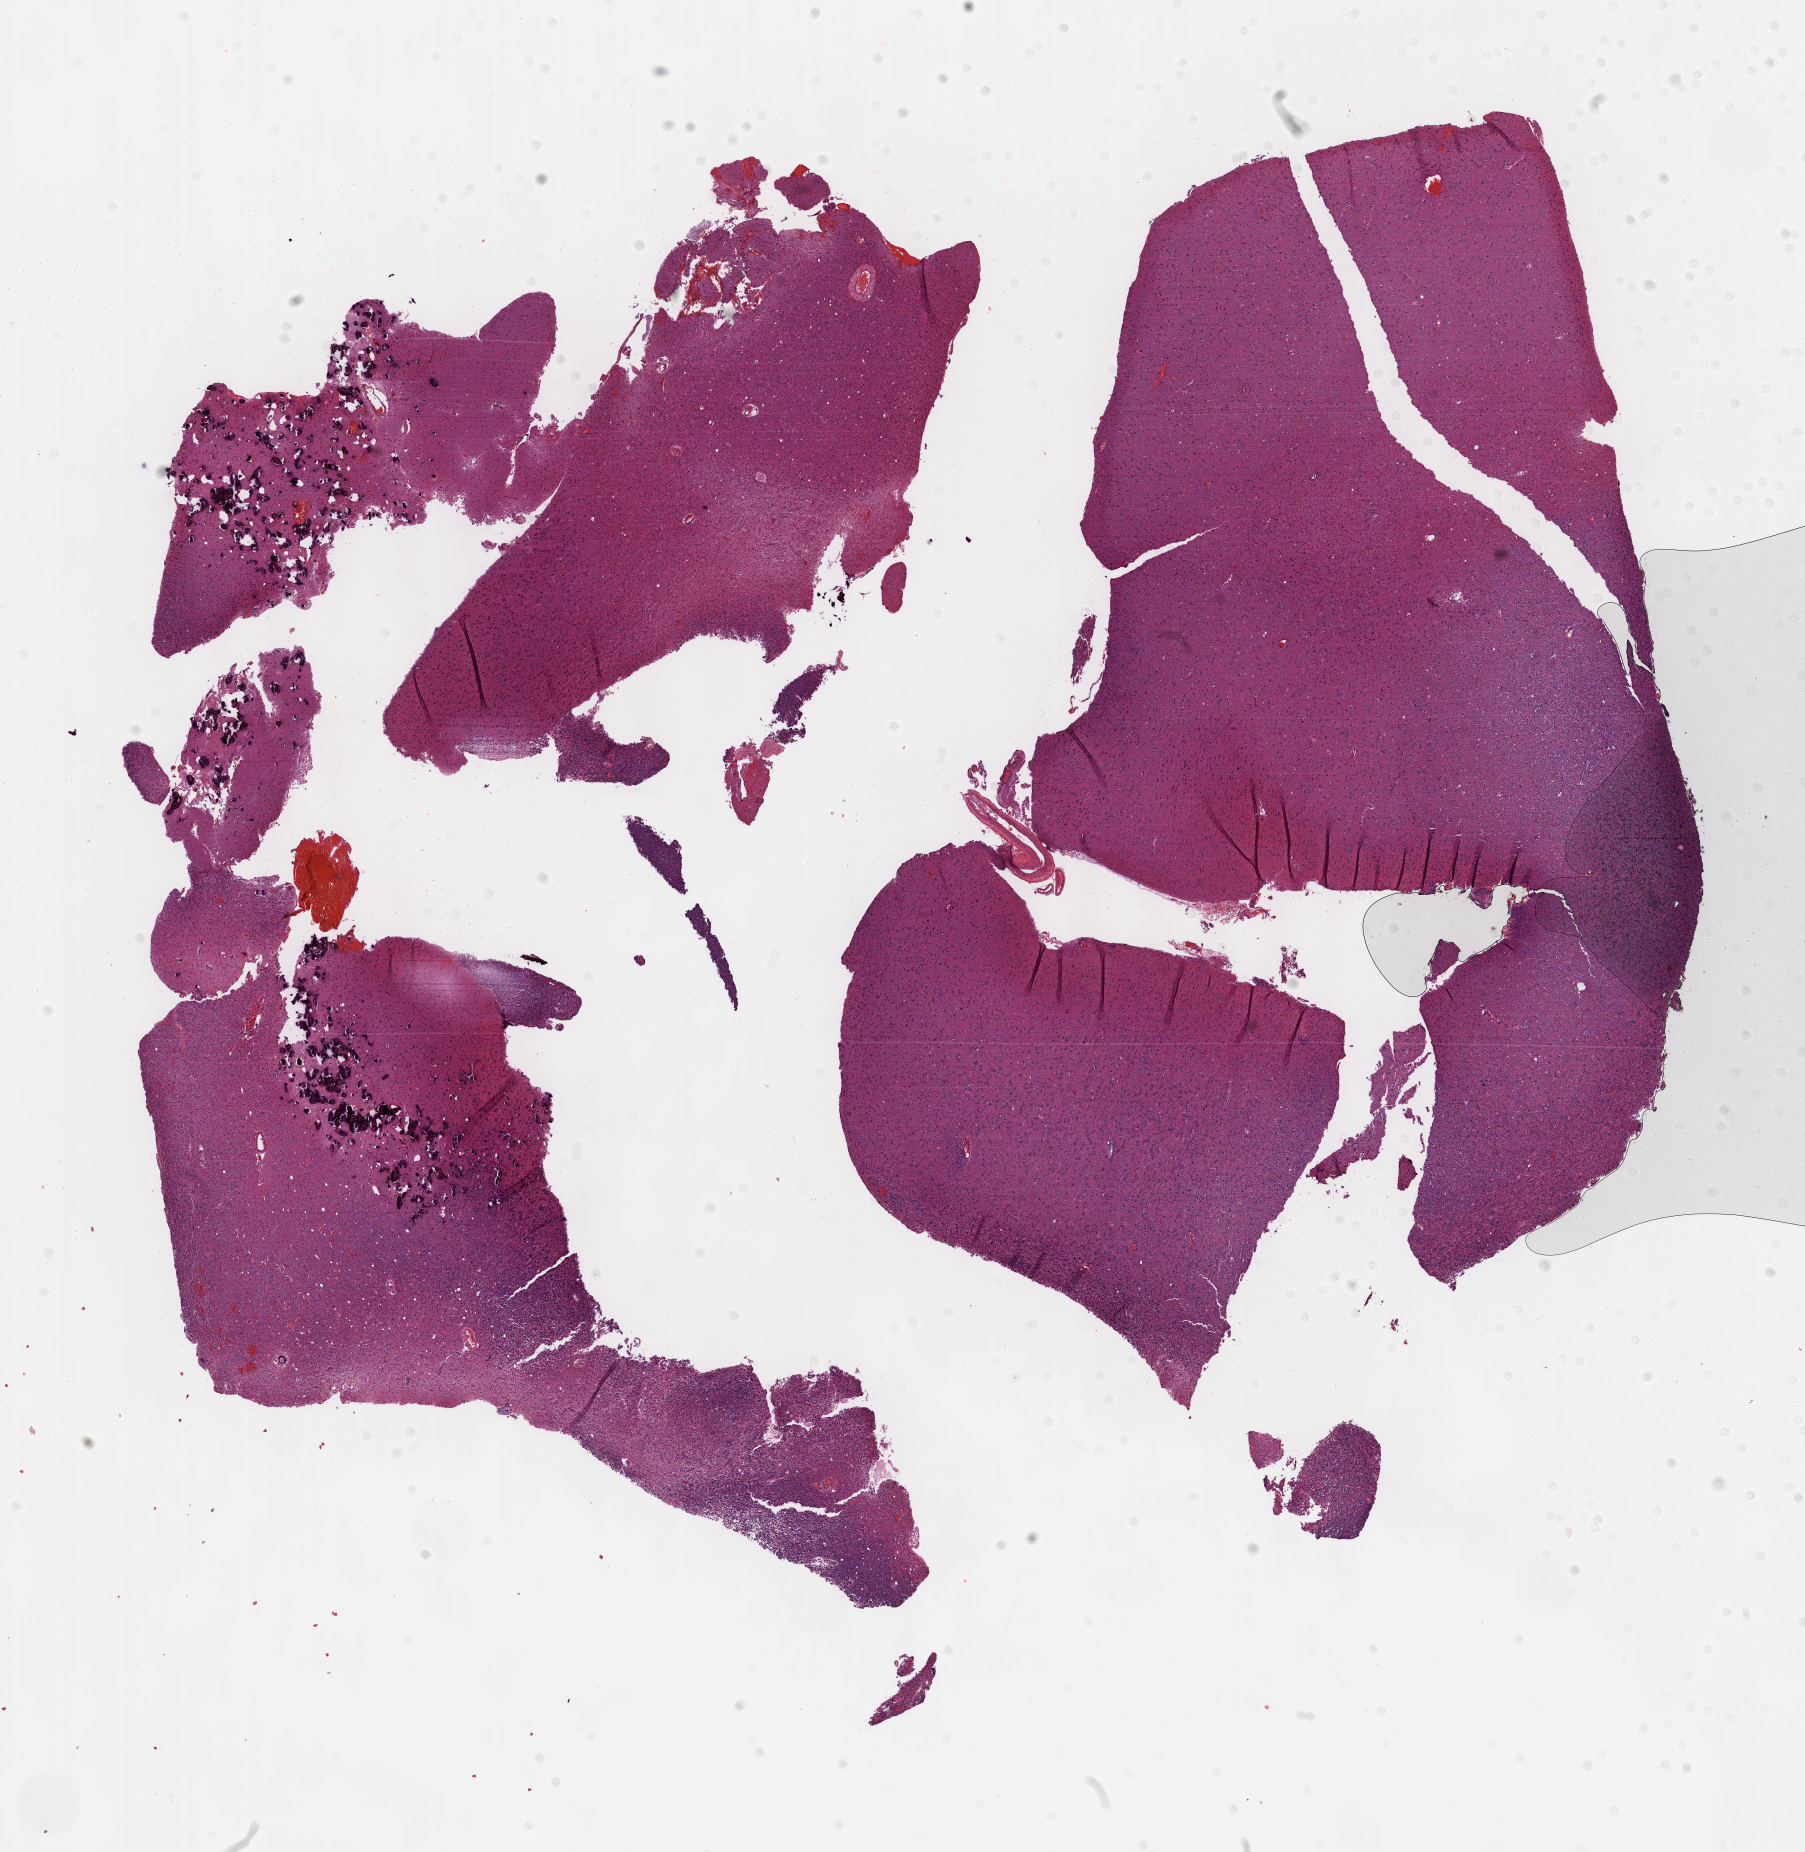
H&E whole-slide image, whole scanned area (about 14.6 x 15.0 mm, slide scanned at 40x) shown as a low-resolution overview, FFPE section, sample: primary tumour, brain. Male, age 39 years at initial diagnosis. Histologic grade: G2 (moderately differentiated).
Histologic diagnosis: Oligodendroglioma, NOS.